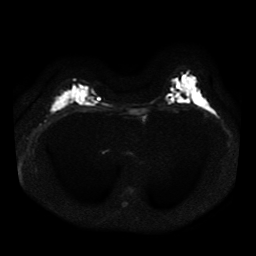
Breast MRI, one axial slice. Position 26 of 41 along the scan axis. Diffusion-weighted series; image 2 of 4 stored at this slice position (different b-values; order by instance number). 1.5 T. 5 mm slice thickness. 256 × 256 image matrix. Female patient.
Structures marked on this image (manually delineated by an expert):
- tumour on diffusion-weighted imaging: box from (x=54, y=90) to (x=69, y=109) px